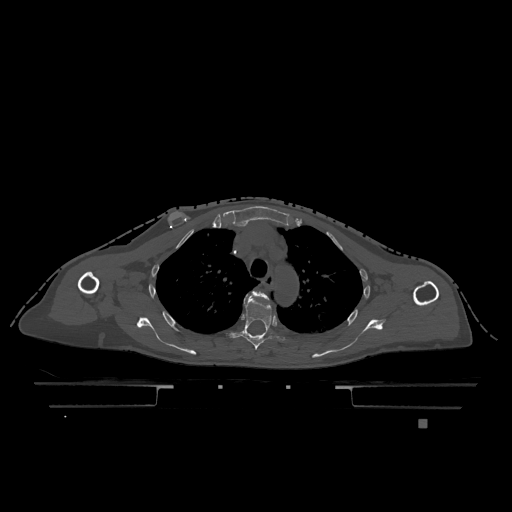
CT including the spine, one axial slice. Bone window (W 1800 / L 400 HU). 0.5 mm slice thickness. 512 × 512 image matrix, field of view 500 × 500 mm. Patient: female, 74 years. Case-level facts recorded for this patient, not image findings: primary cancer: lung.
Outlined on this slice (semi-automatically segmented with operator editing):
- T3 vertebra: bounding box (x1, y1, x2, y2) in pixels: (246, 291, 269, 299)
- T4 vertebra: (226, 297, 286, 350)